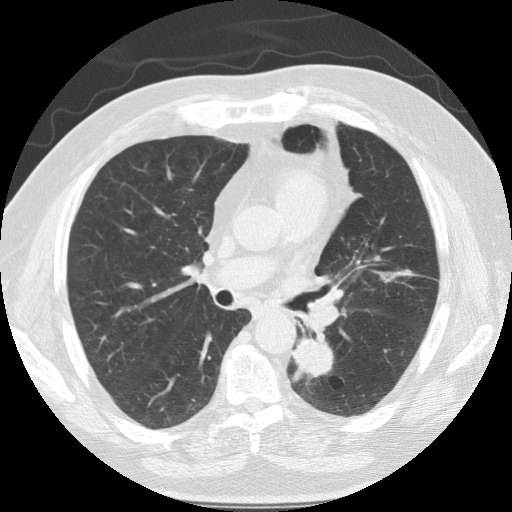
Axial slice from a low-dose chest CT screening exam. Baseline annual screen. Lung window (W 1500 / L -600 HU). 2.5 mm slice thickness. Slice 57 of 124 in the series. Male, age 68 years at enrolment. Former smoker at enrolment.
Lesion marked by an expert reader, bounding box (x1, y1, x2, y2) in pixels: (279, 317, 352, 396). The screening reader recorded 3 non-calcified nodules or masses ≥4 mm on this exam; which of them this box marks is not recorded. Official screen result: positive, change unspecified: nodule(s) >= 4 mm or enlarging nodule(s), mass(es), or other non-specific abnormalities suspicious for lung cancer.